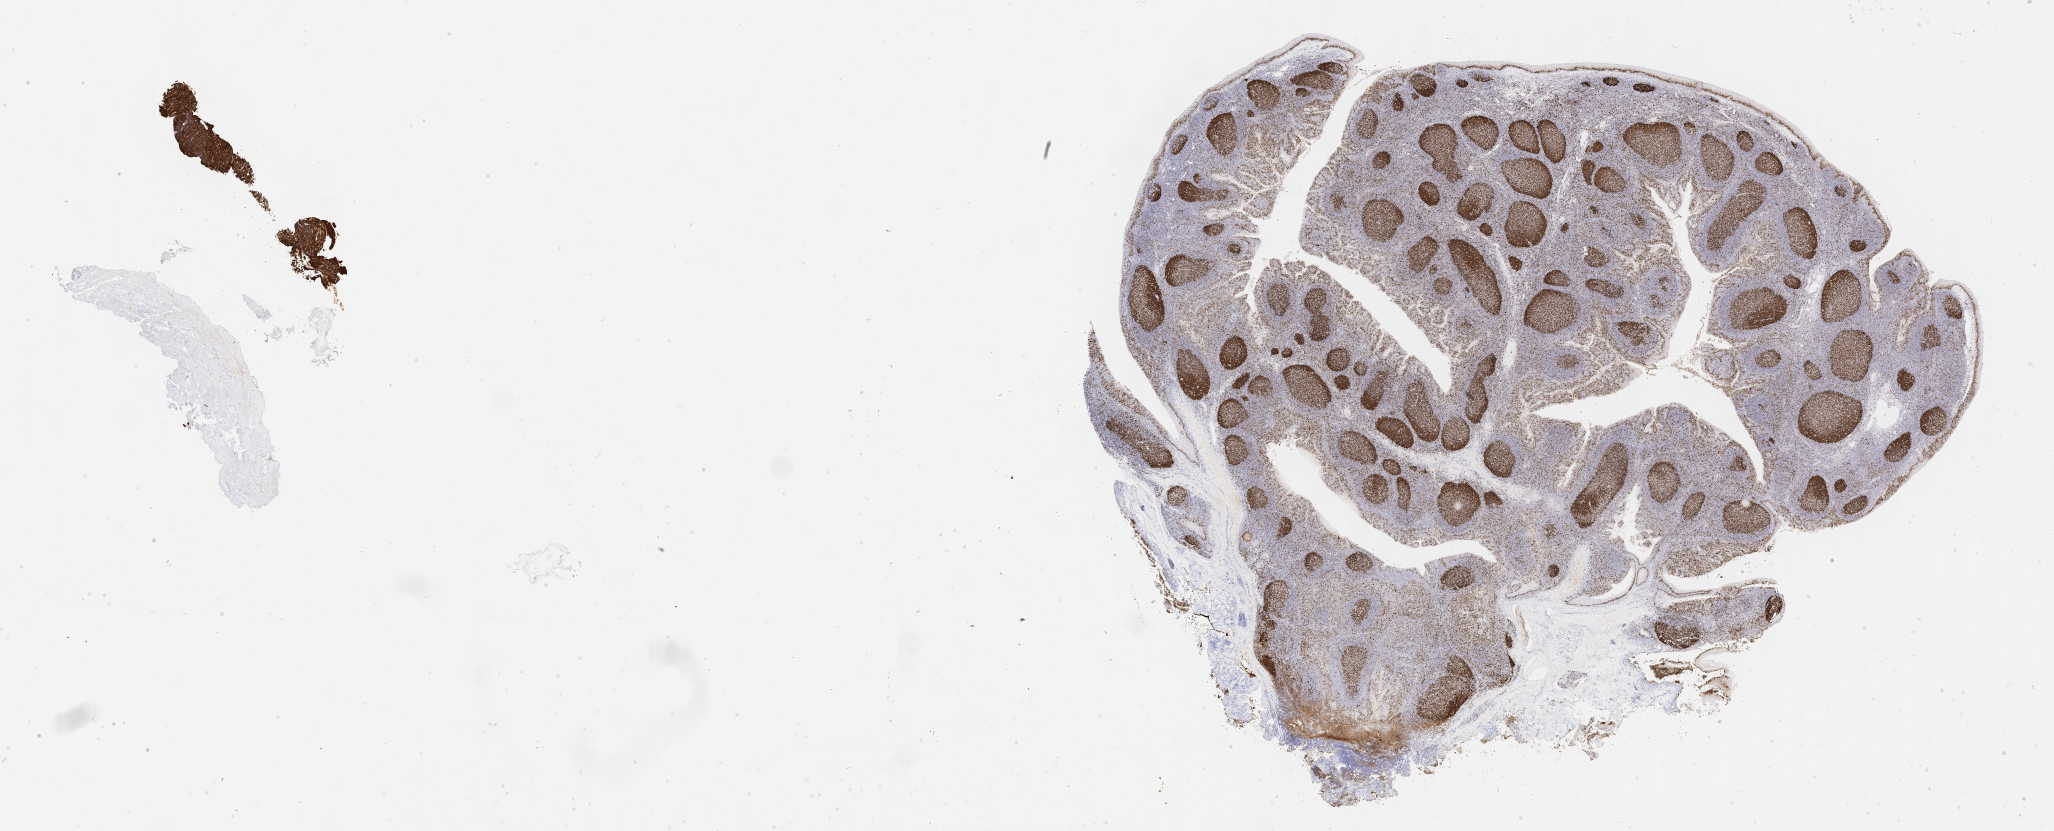
Whole-slide image, immunohistochemical stain for Ki-67 — whole scanned area (about 33.2 x 13.4 mm) shown as a low-resolution overview, specimen: tumor tissue, anatomic site: liver. Male patient.
• diagnosis: Burkitt lymphoma, NOS